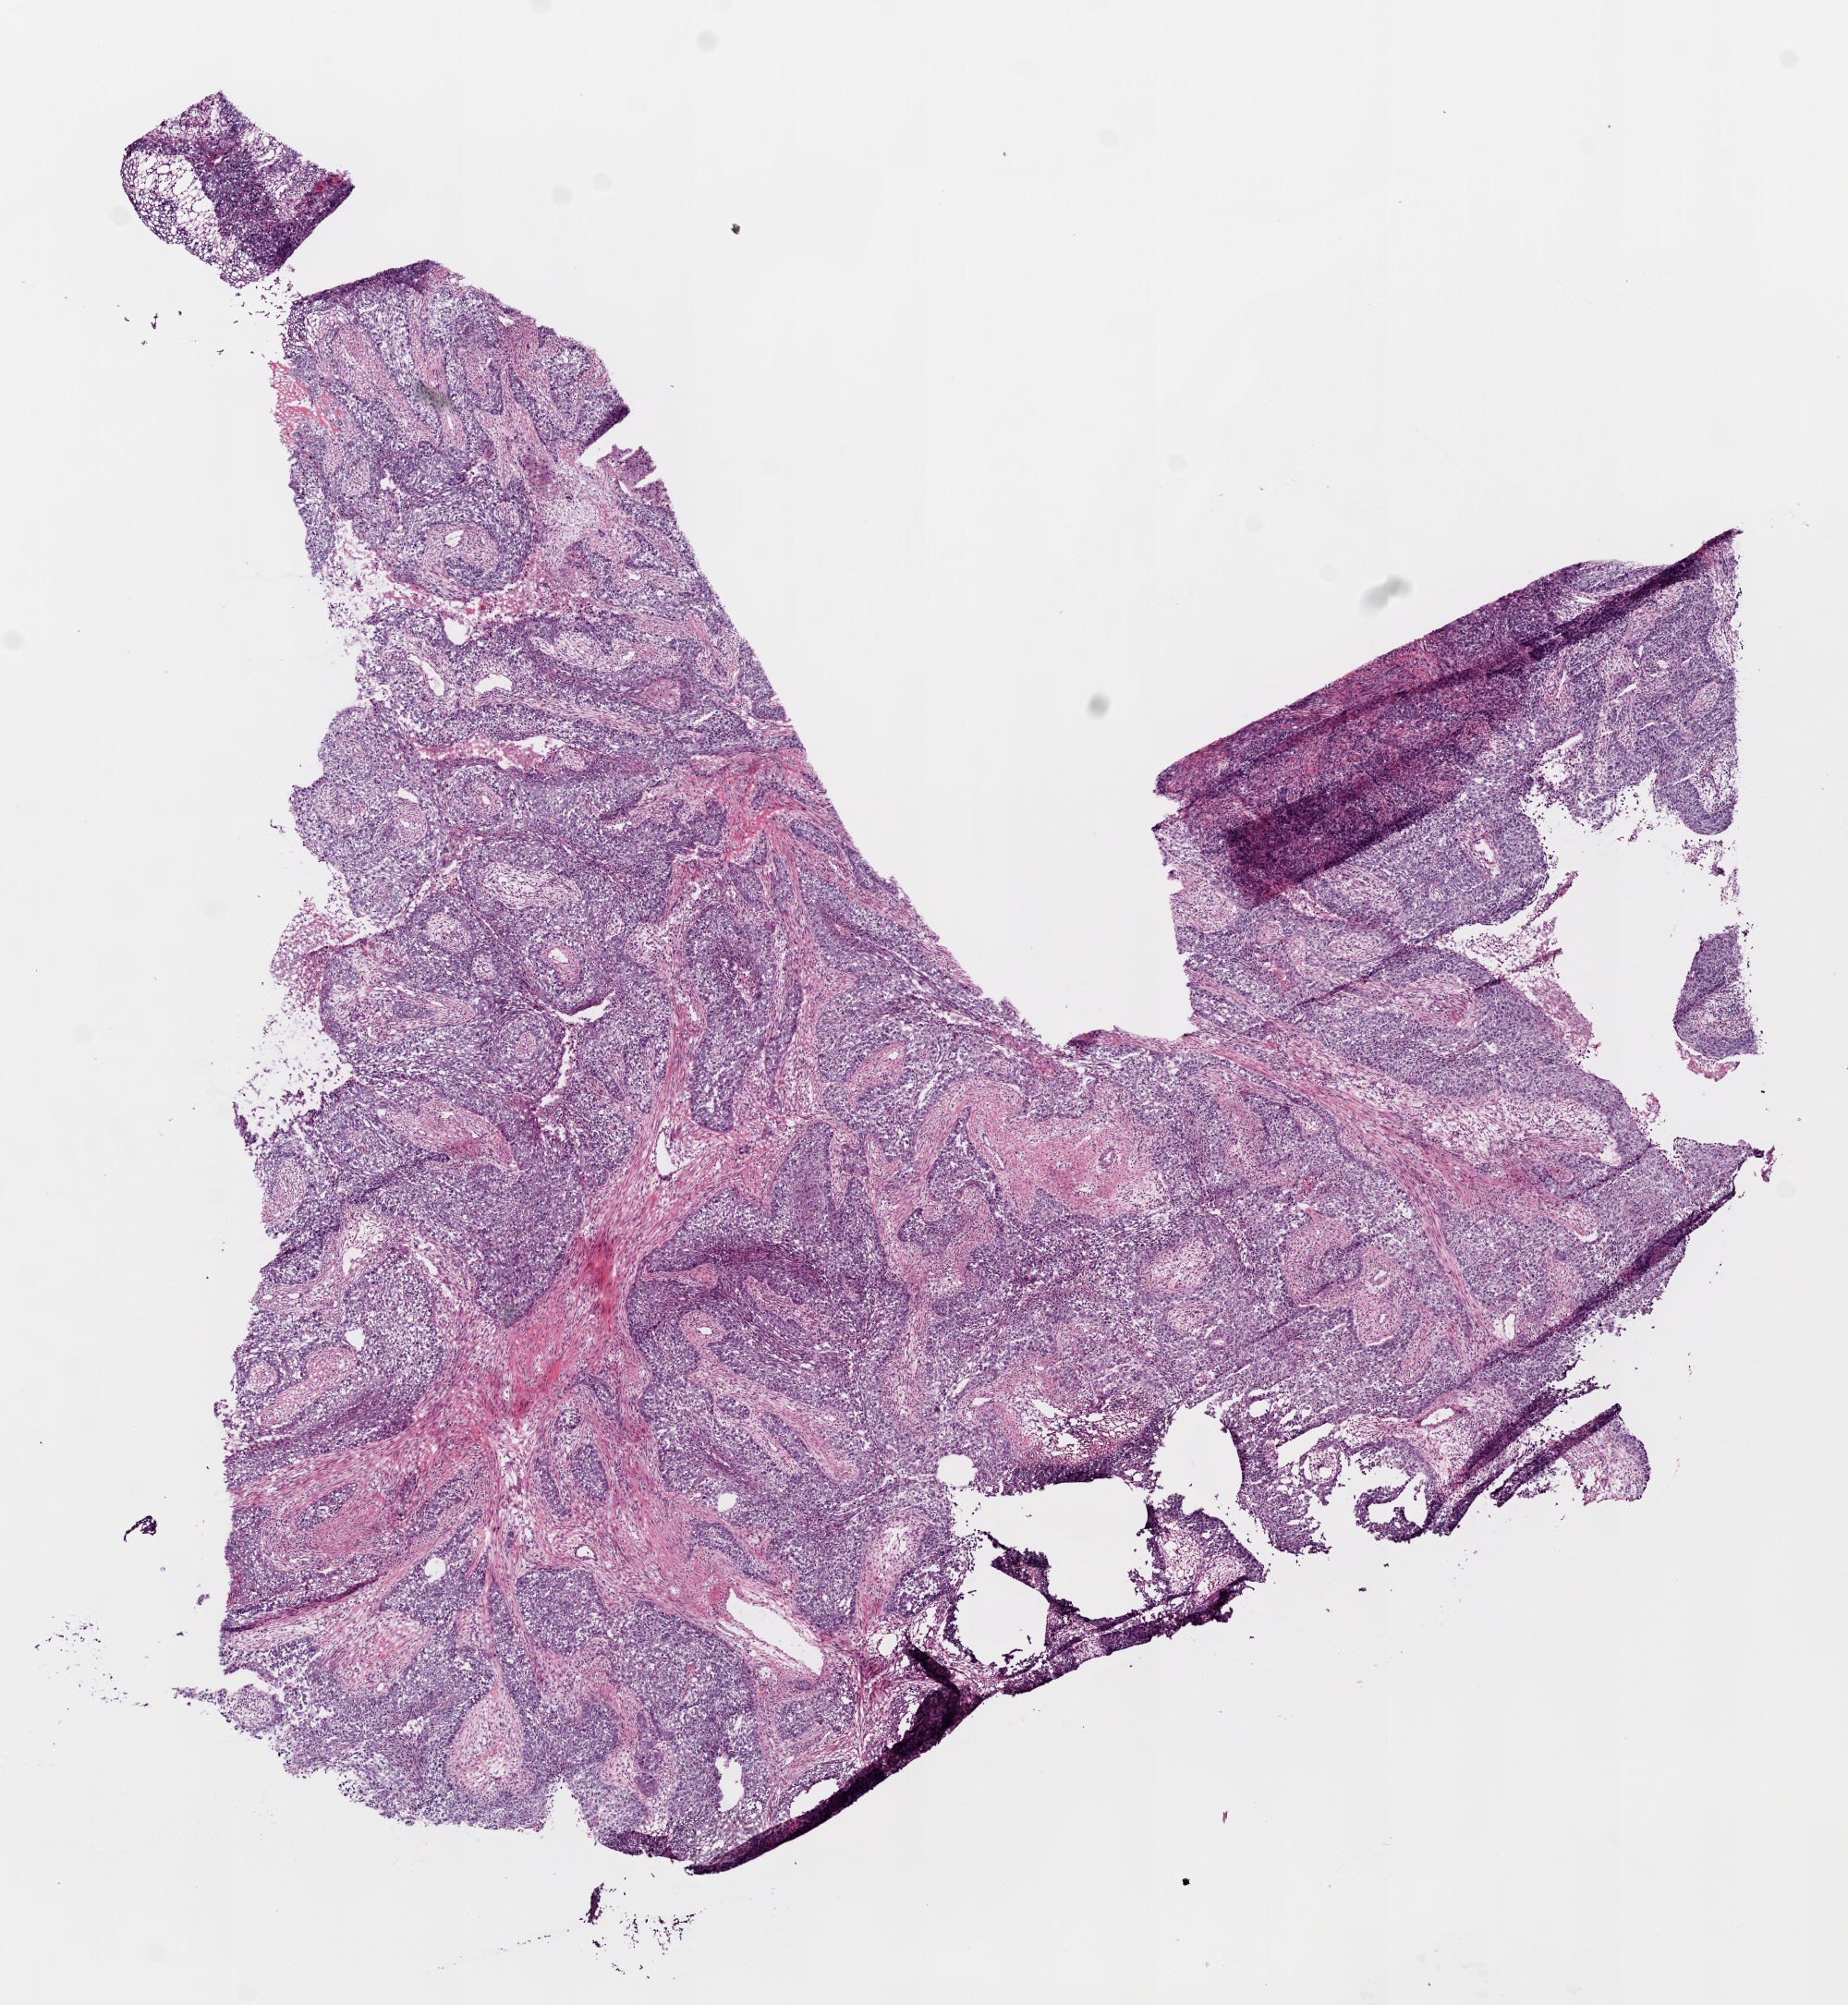
Whole-slide histology image, Hematoxylin and eosin (H&E) stained — shown as a low-resolution overview of the whole scanned area (about 8.0 x 8.7 mm, acquisition: 20x scan). Frozen section. Sample: primary tumour, lung. Male, age 77 years at initial diagnosis. Slide review estimates, as recorded: tumour cells 70%, tumour nuclei 75%, normal cells 0%, stromal cells 20%, necrosis 10%.
* AJCC pathologic stage: IIA (7th edition)
* TNM: T2b N0 M0
* laterality: right
* pathologic diagnosis: Squamous cell carcinoma, NOS (lower lobe, lung)